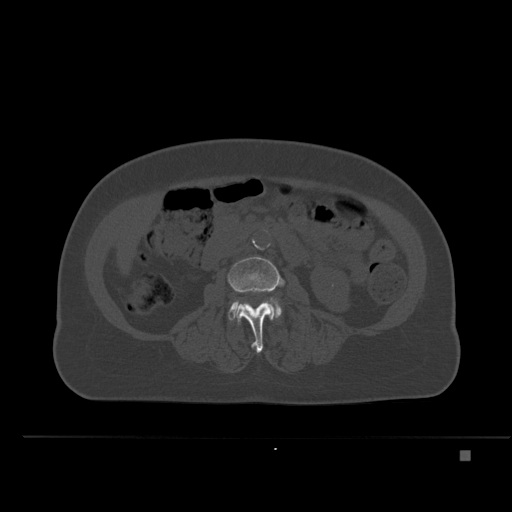
CT including the spine, one axial slice. Position 193 of 477 along the scan axis. Bone window (W 1800 / L 400 HU). 1.5 mm slice thickness. 512 × 512 image matrix, field of view 422 × 422 mm. Patient: female, 74 years. From the clinical record (not read from this slice): primary cancer: colon.
Annotated regions visible in this slice (semi-automatically segmented with operator editing):
- L3 vertebra: bounding box [x1, y1, x2, y2] px = [228, 257, 283, 353]
- L4 vertebra: [229, 298, 282, 320]